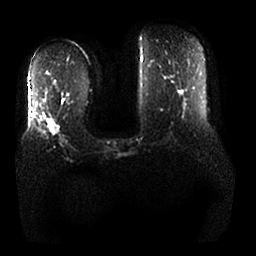
Breast MRI, one axial slice. Position 11 of 25 along the scan axis. Diffusion-weighted series; image 2 of 4 stored at this slice position (different b-values; order by instance number). 1.5 T. 4 mm slice thickness. 256 × 256 image matrix, field of view 380 × 380 mm. Female patient.
Outlined on this slice (expert manual segmentation):
- tumour on diffusion-weighted imaging: bounding box <48,119,60,135> (left, top, right, bottom; pixels)